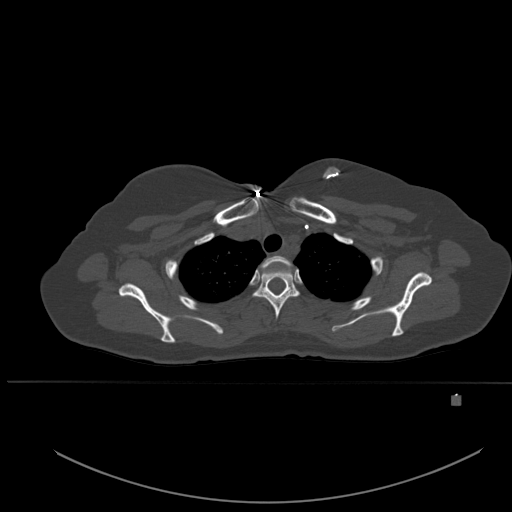
CT including the spine, one axial slice; slice 407 of 651 in the series (ordered by position); bone window (W 1800 / L 400 HU); 1.5 mm slice thickness; 512 × 512 image matrix, field of view 443 × 443 mm. Female patient, age 49 years. Case-level facts recorded for this patient, not image findings: primary cancer: breast; vertebrae with lytic lesions (as recorded): L3, T12, L4.
Annotated regions visible in this slice (semi-automatically segmented with operator editing):
- T1 vertebra: bounding box (x1, y1, x2, y2) in pixels: (261, 256, 291, 272)
- T2 vertebra: (253, 267, 299, 320)